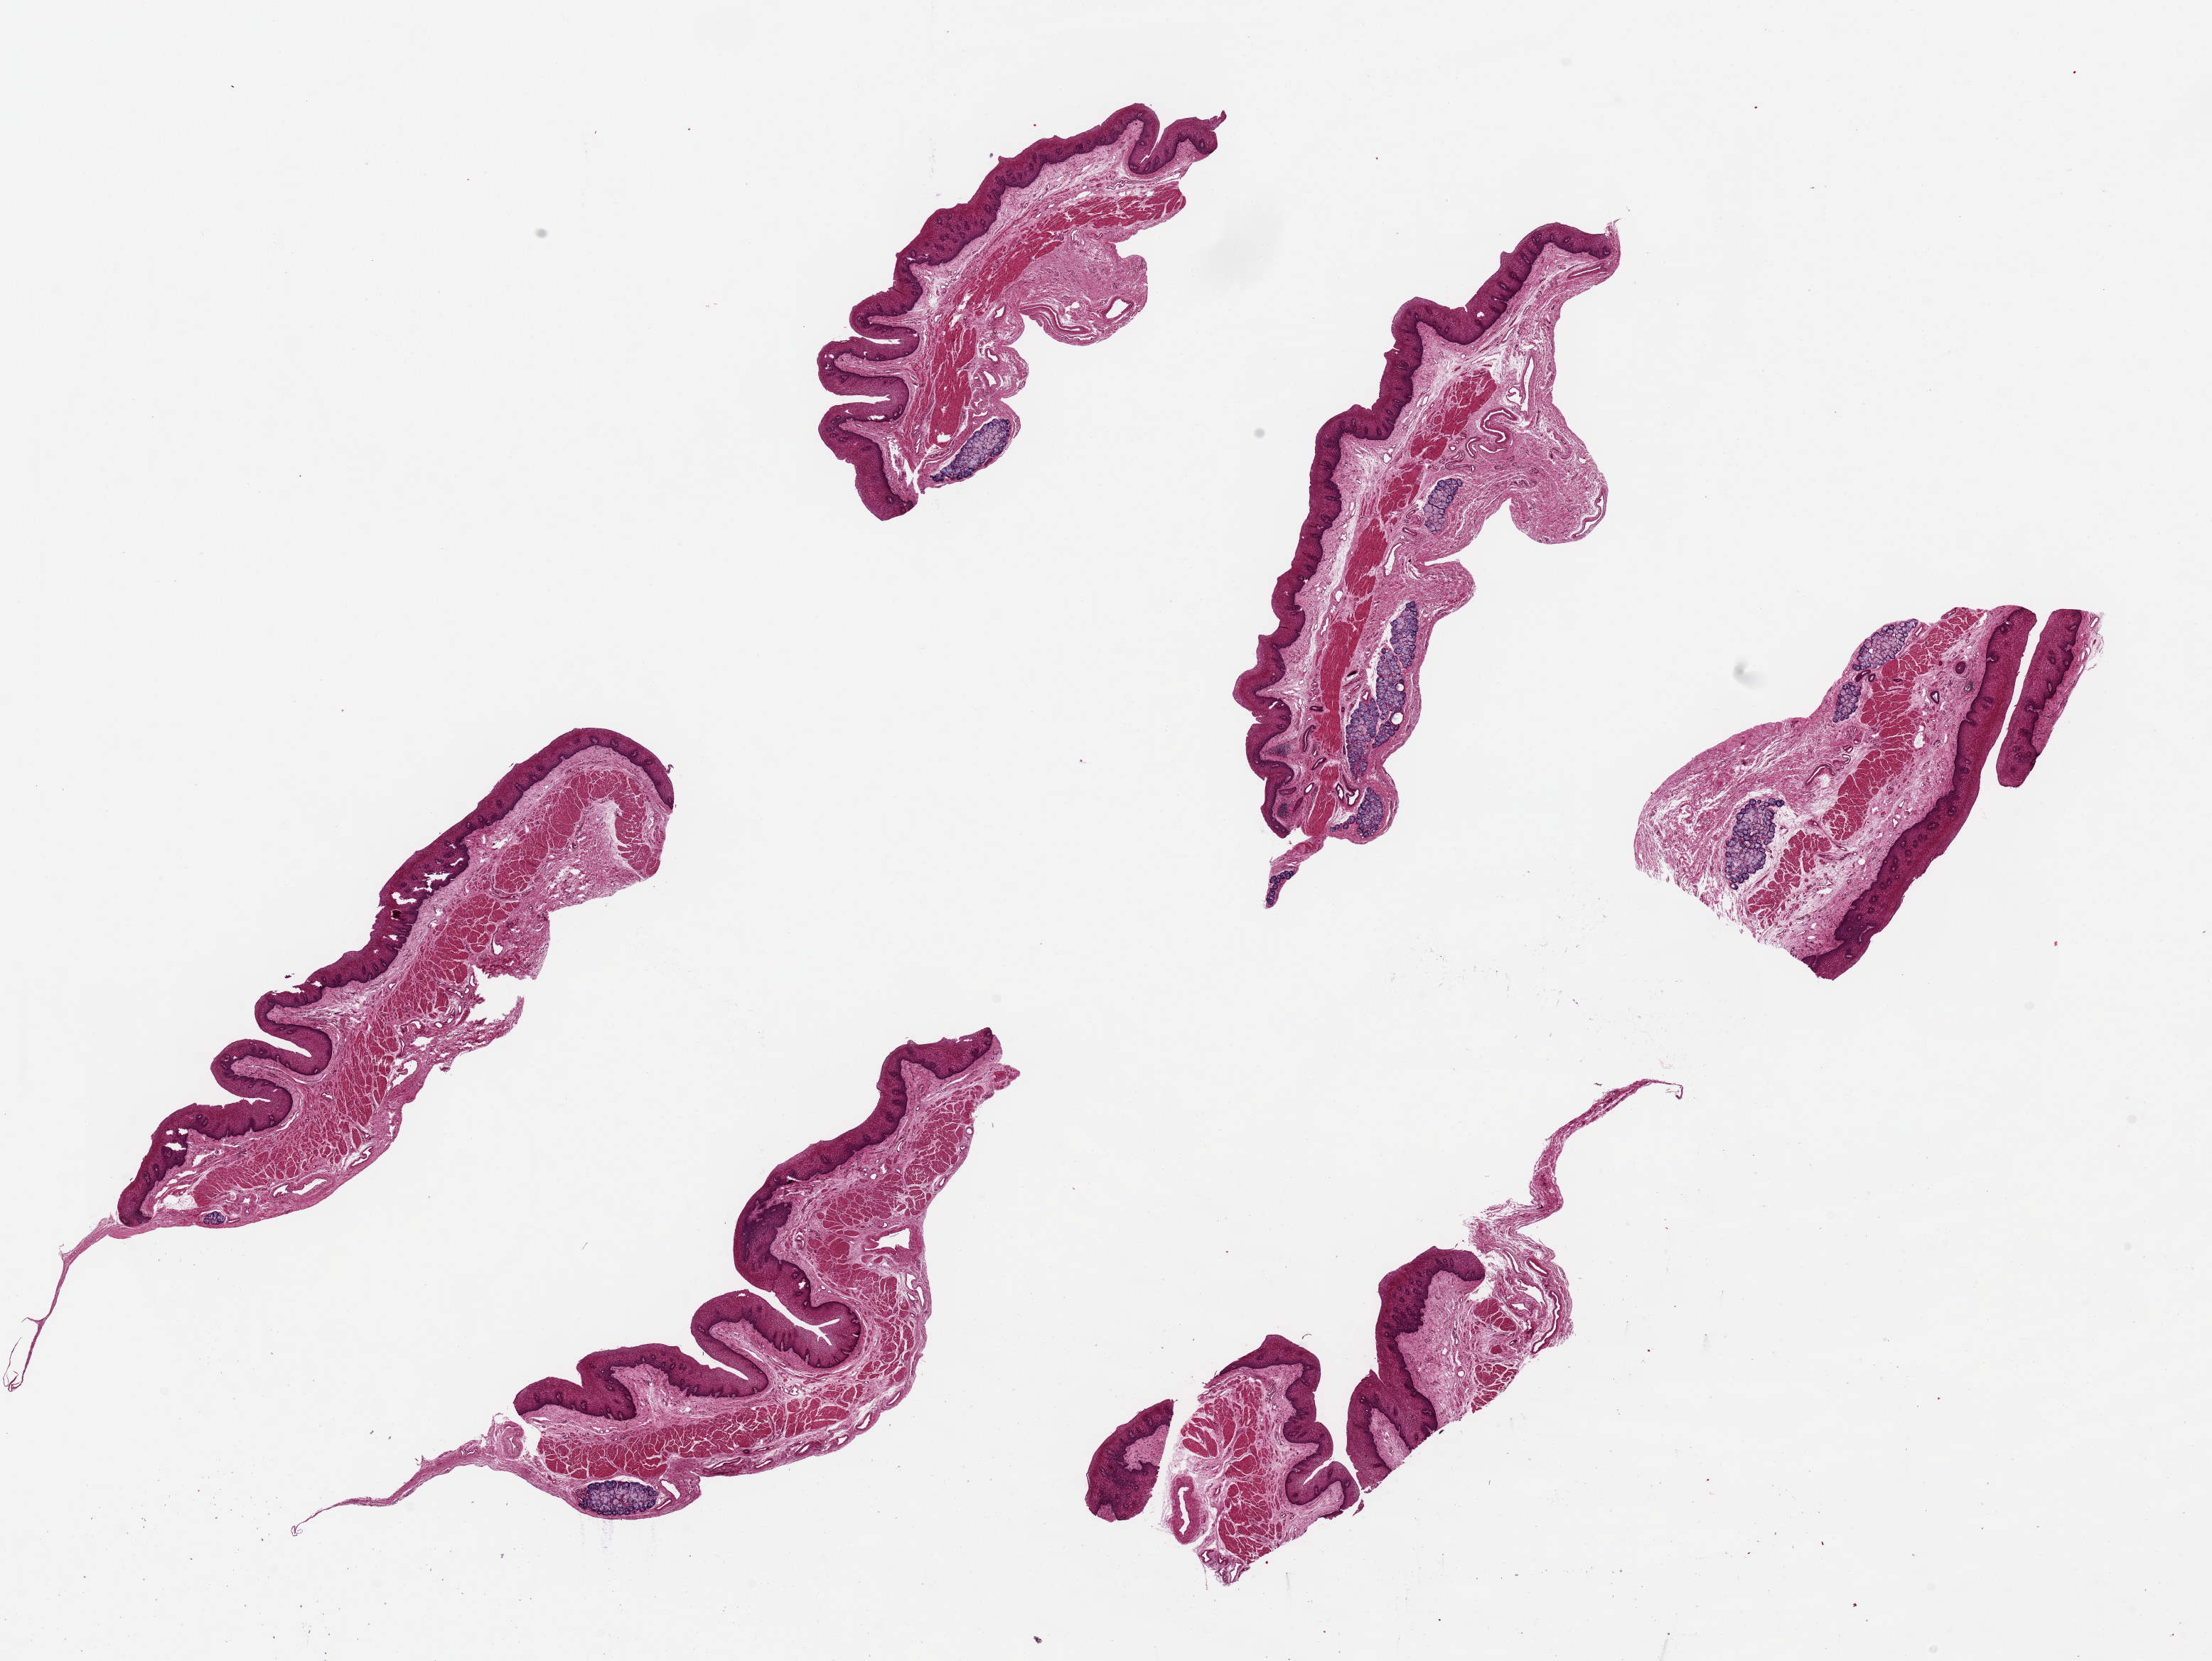
Hematoxylin and eosin (H&E) whole-slide image — a low-resolution overview of the entire scanned area, about 24.6 x 18.5 mm. PAXgene-fixed paraffin-embedded (PFPE) section. Section of esophageal mucous membrane (target tissue). Tissue donor sample. Donor: female.
Review note (as recorded): 6 pieces, ~7x2mm. Squamous mucosa is ~20% of thickness. Numerous mucosal mucus glands noted.